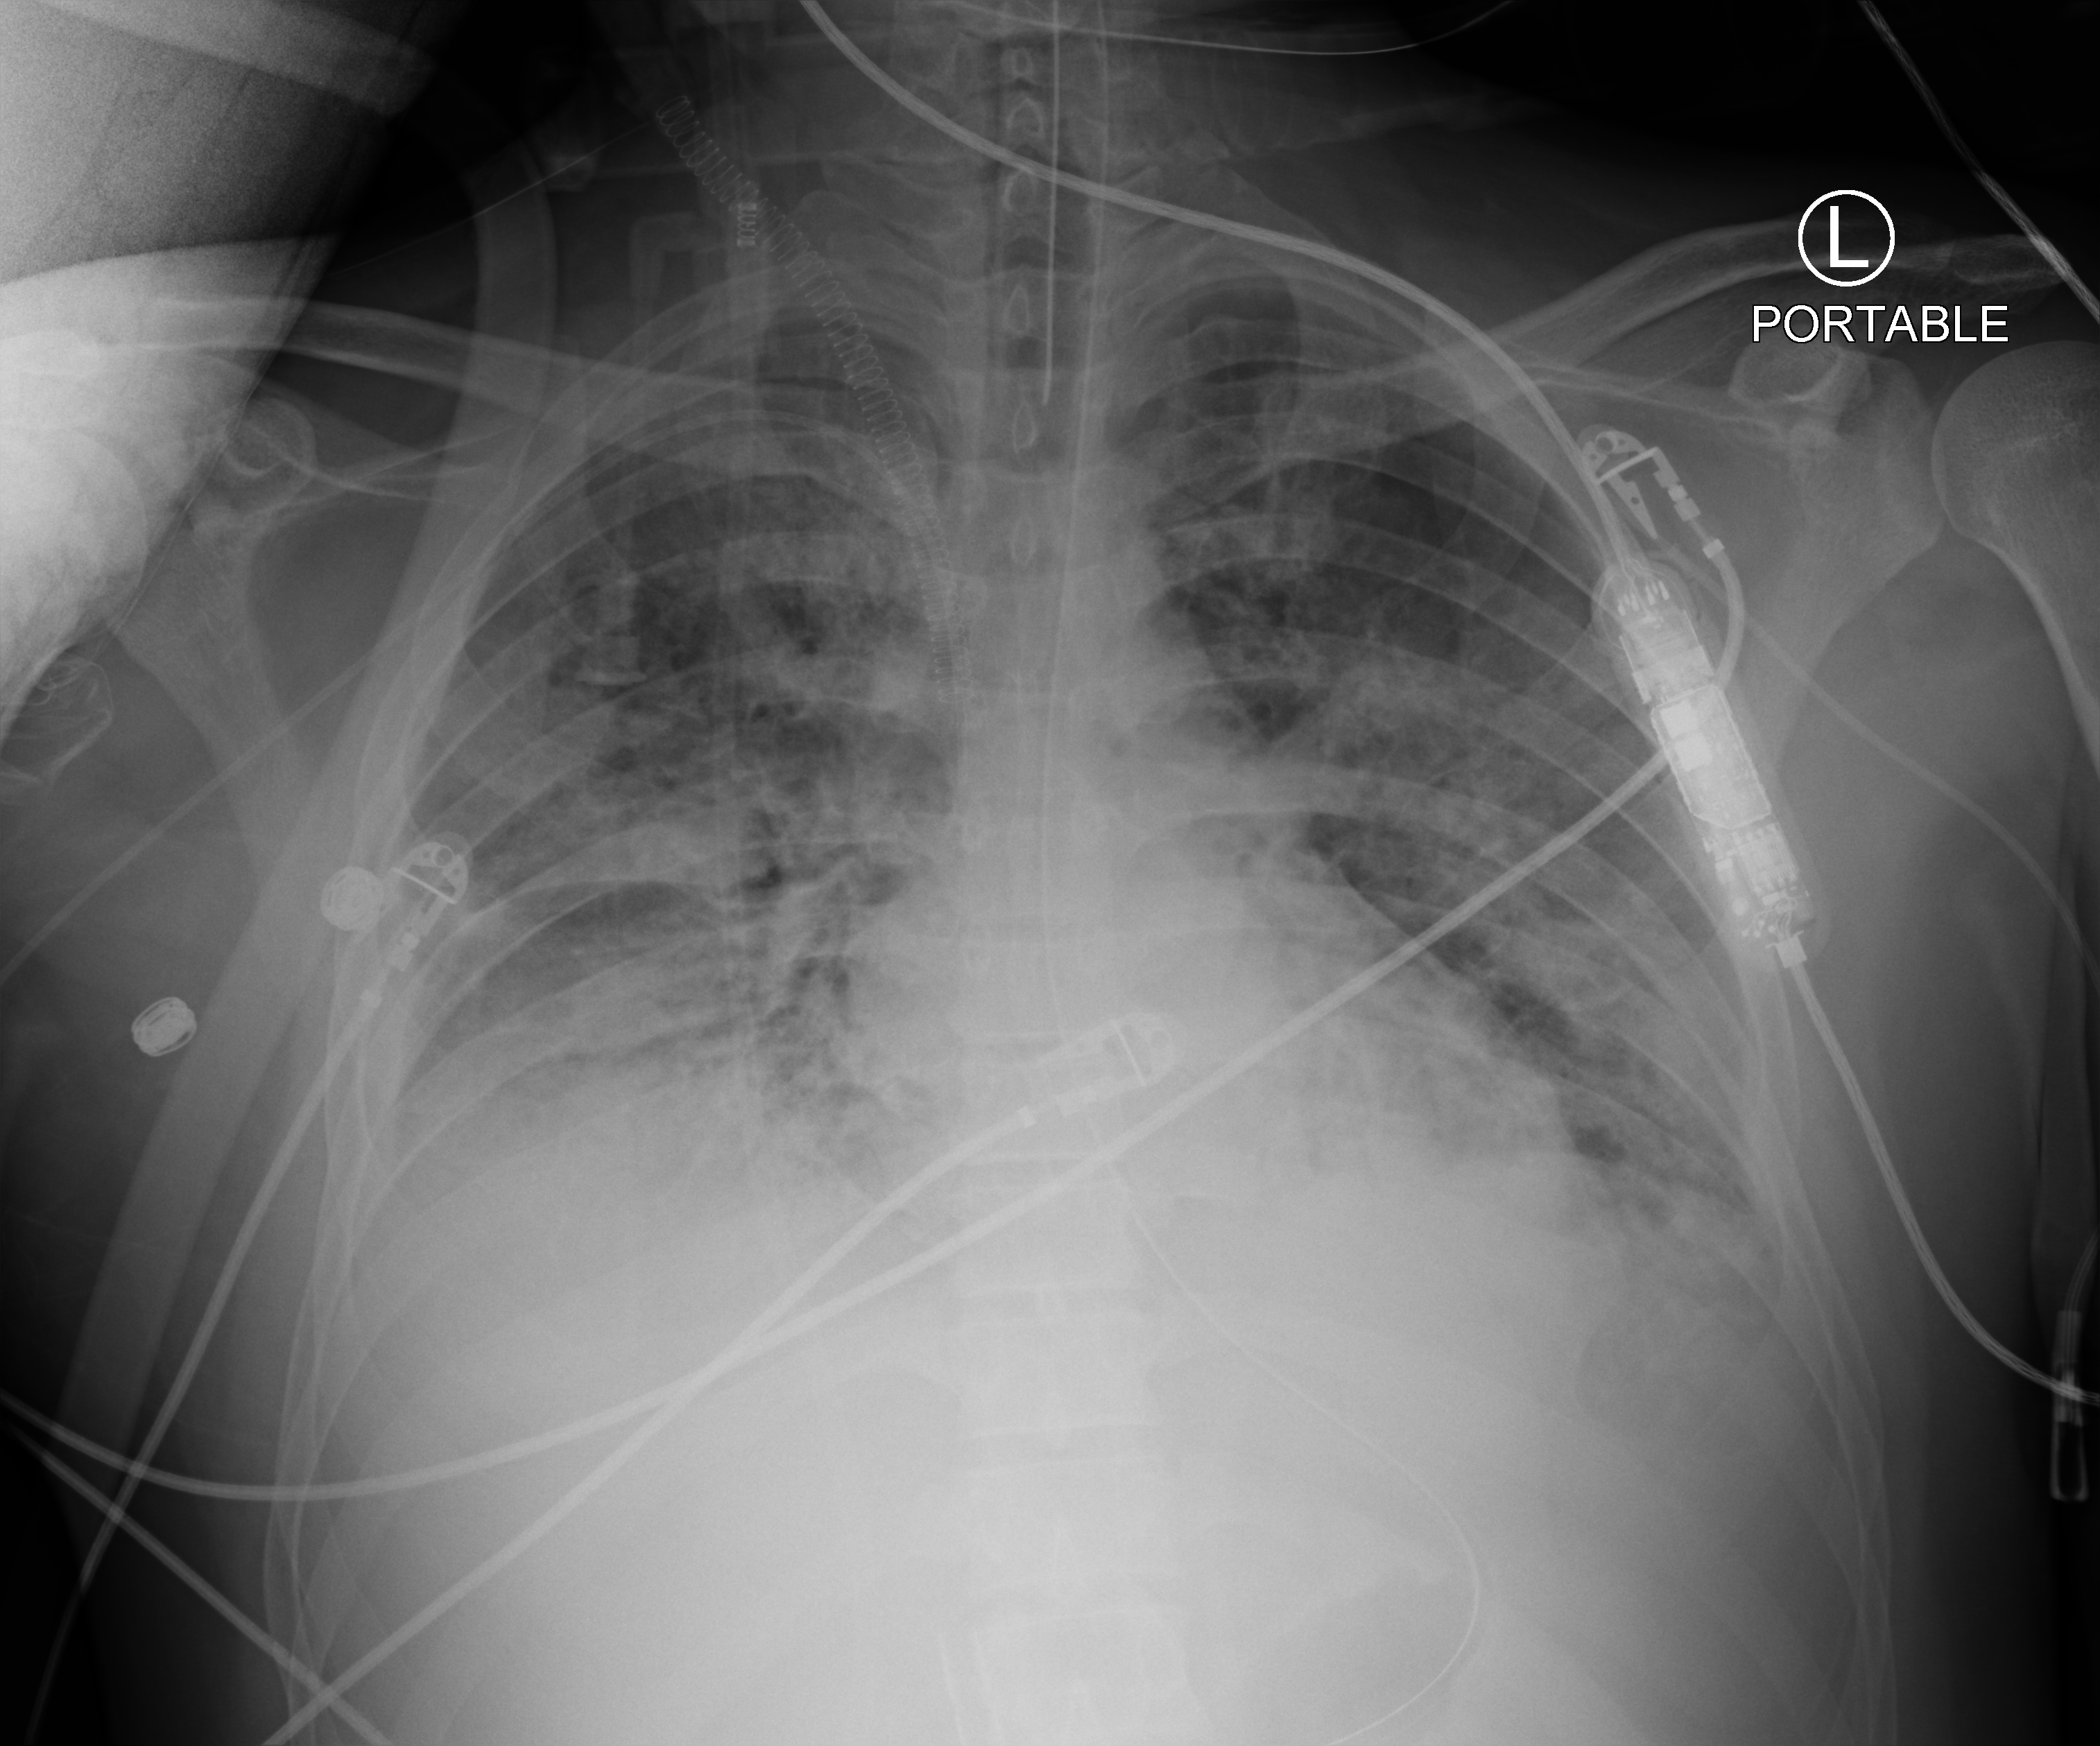
Bedside chest radiograph (computed radiography); anteroposterior (AP) projection. Patient hospitalised with COVID-19, aged 18–59 years.
Admission-level facts for this patient (not findings on this image; timing relative to this image not recorded): admitted to intensive care during this hospital stay: yes; mechanically ventilated during this hospital stay: yes.